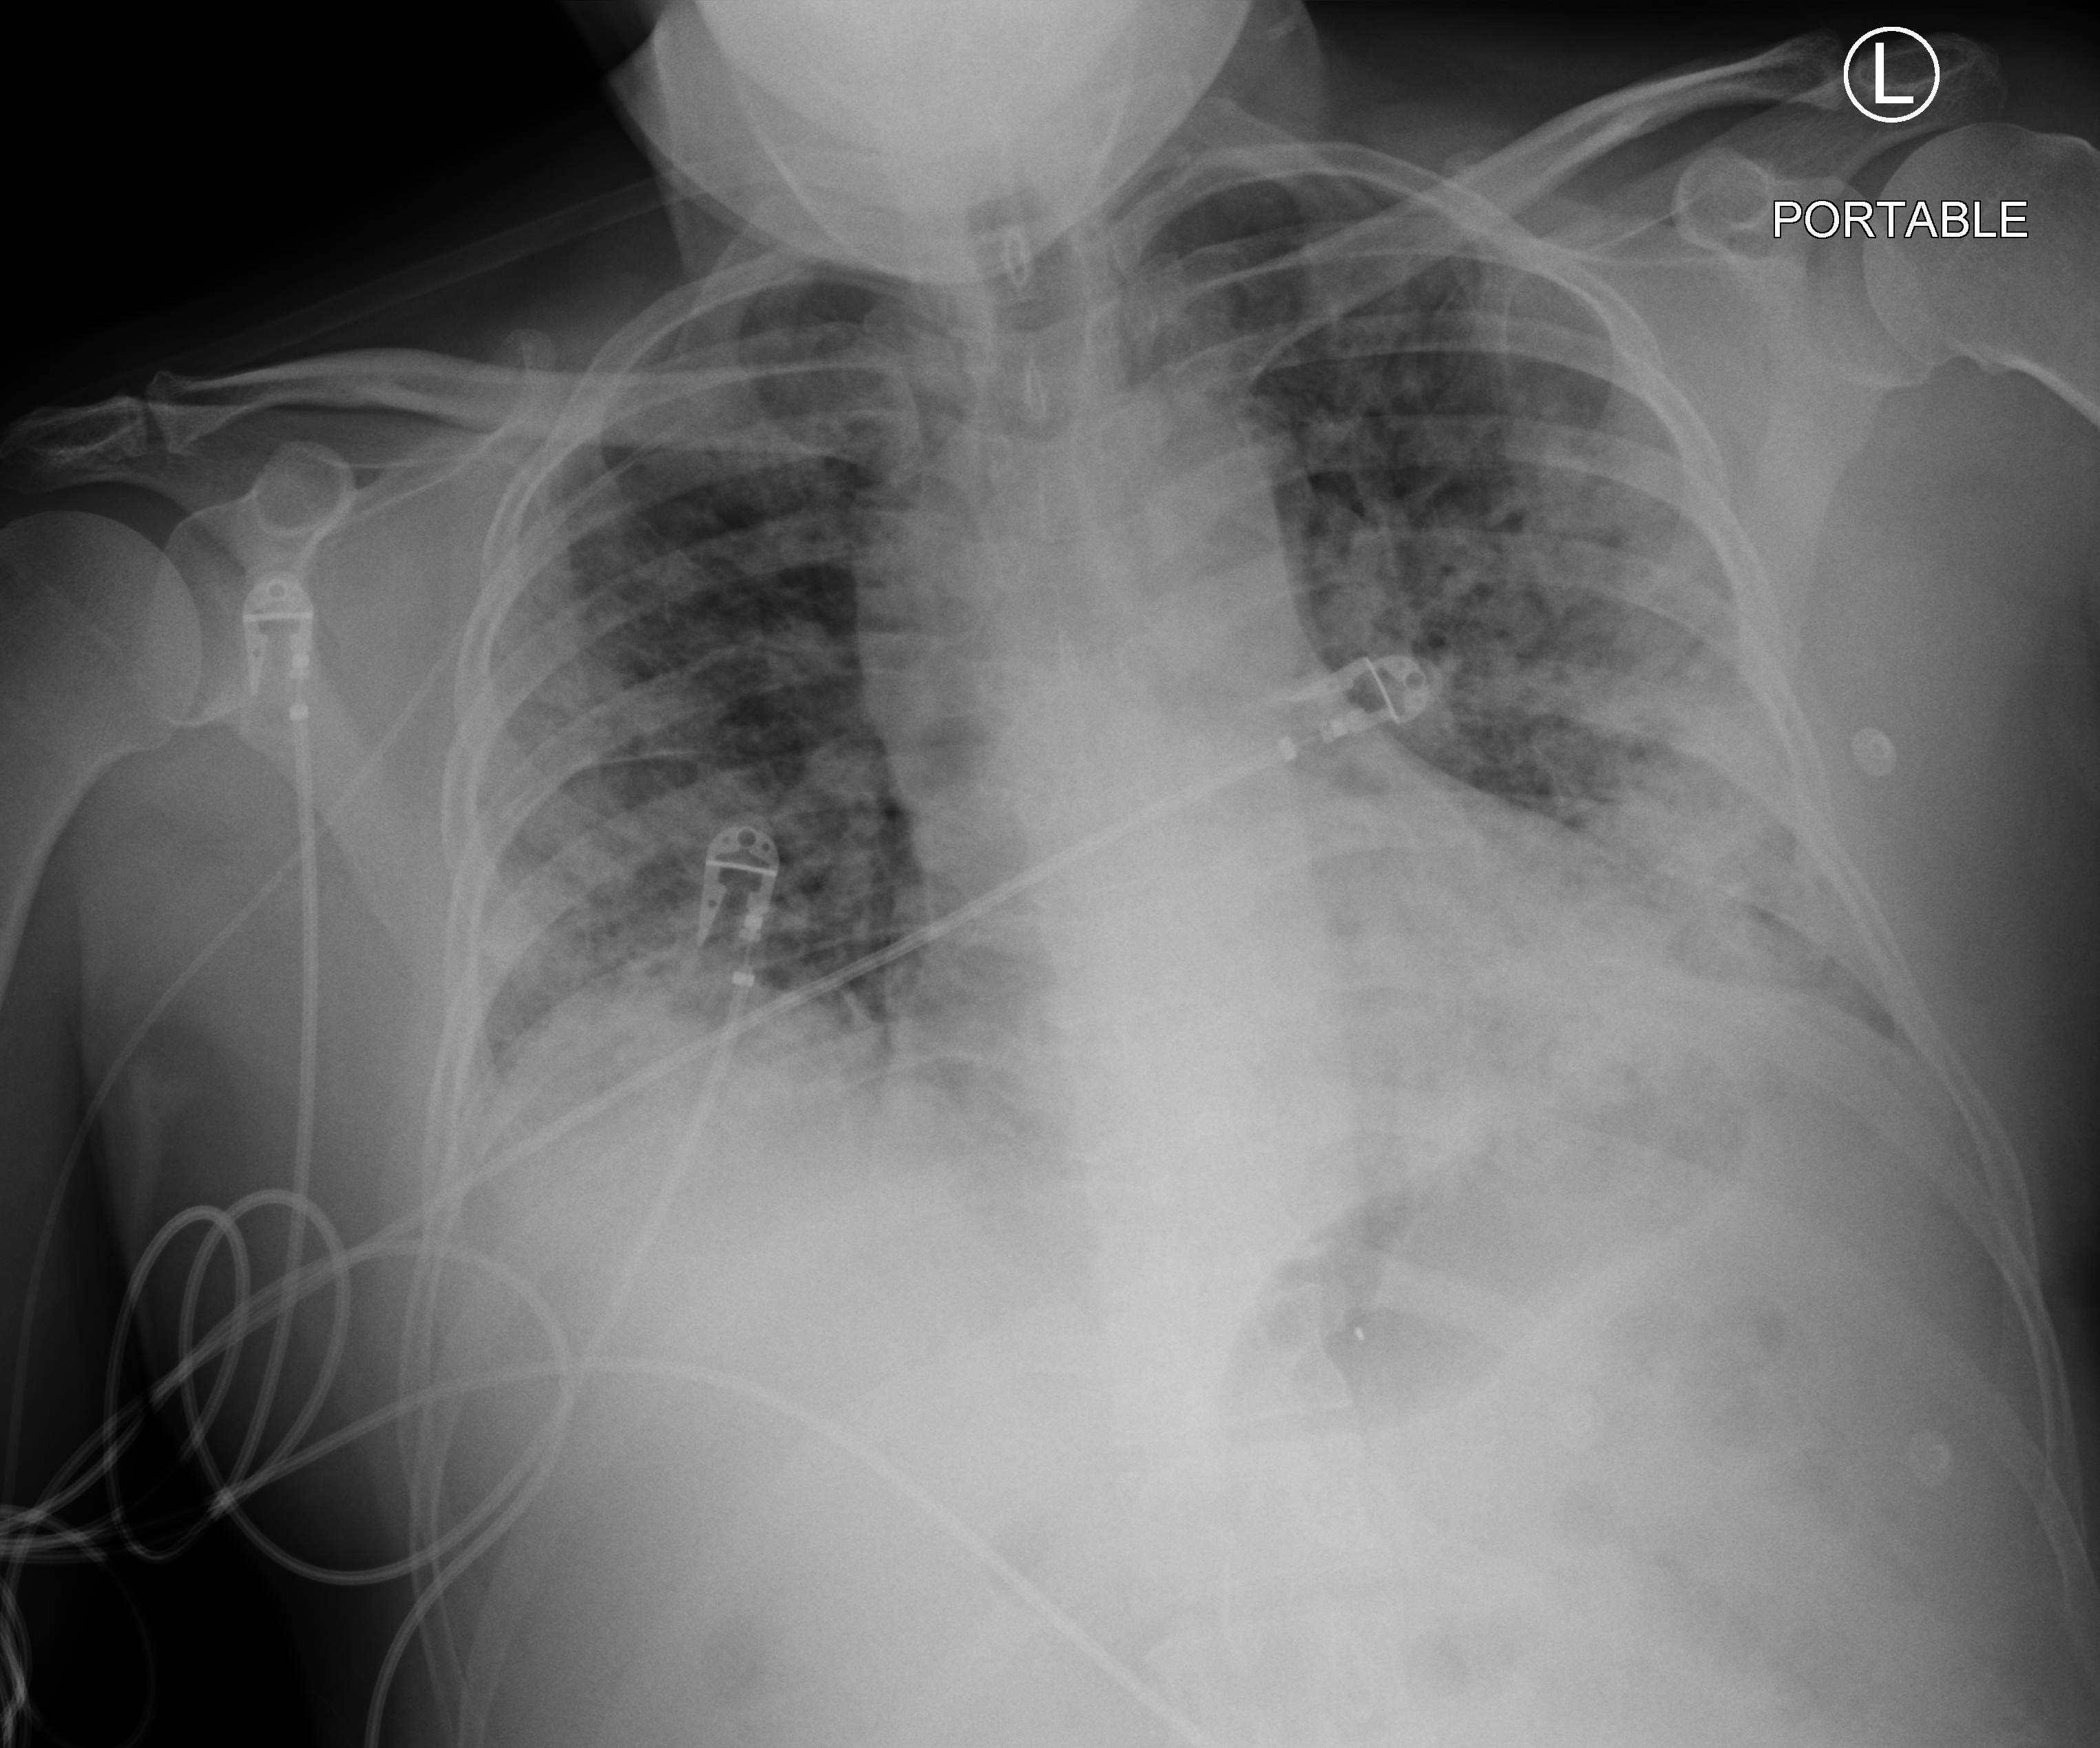
Chest X-ray (portable); anteroposterior (AP) projection. Male patient hospitalised with COVID-19, age 18–59 years.
Hospital-stay facts (about this admission, not read from this image; timing relative to this image not recorded):
- chronic kidney disease (admission record): no
- mechanically ventilated during this hospital stay: no